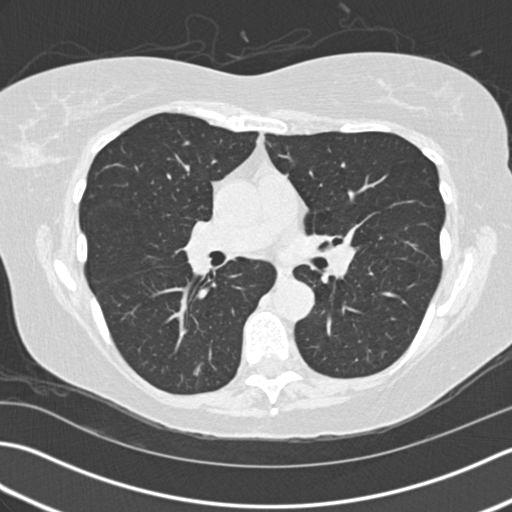
Chest CT (low-dose screening protocol), one axial image, third annual screen, lung window (W 1500 / L -600 HU), standard (soft-tissue) reconstruction kernel (B30f). Female participant, aged 60 years at enrolment. Former smoker at enrolment.
• Expert-annotated lung lesion, bounding box <176,351,222,398> (left, top, right, bottom; pixels).
• The screening reader recorded 3 non-calcified nodules or masses ≥4 mm on this exam (right lower lobe, right middle lobe, right middle lobe); which of them this box marks is not recorded.
• Official screen result: positive, other.